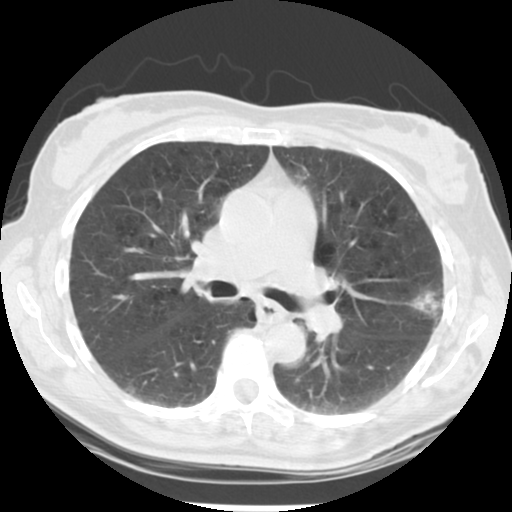
Chest CT (low-dose screening protocol), one axial image, second screening round (one year after baseline), lung window (W 1500 / L -600 HU), 2.5 mm slice thickness, slice 131 of 223 in the series. Female participant, aged 61 years at enrolment. Current smoker at enrolment.
• Lesion marked by an expert reader, bounding box <404,277,464,338> (left, top, right, bottom; pixels).
• Reader record for this screening exam (exam-level; its link to the box is not recorded): non-calcified nodule or mass ≥4 mm, left upper lobe, 15 × 15 mm, poorly defined margins, mixed attenuation, pre-existing on the prior screen: no.
• Participant outcome: lung cancer diagnosed 152 days after this screen — bronchiolo-alveolar adenocarcinoma, NOS, left upper lobe, well differentiated (G1), stage IA (AJCC 6th edition), 11 mm at pathology.